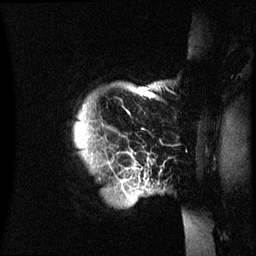
Breast MRI (dynamic contrast-enhanced), one sagittal slice; position 57 of 60 along the scan axis; dynamic contrast-enhanced series, image 2 of 3 at this slice position (ordered by acquisition); 1.5 T; TE 4.2 ms, TR 8.4 ms; 2.4 mm slice thickness; 256 × 256 image matrix, field of view 230 × 230 mm. Female patient, age 48 years.
Outlined on this slice (semi-automatically segmented with operator editing):
- analysis volume of interest (the breast-tissue region the enhancement analysis was run in; not a lesion): box from (x=74, y=84) to (x=193, y=233) px
- tumour enhancement mask (voxels above the 70 % enhancement threshold inside the analysis volume of interest): (x=122, y=88)–(x=145, y=182)